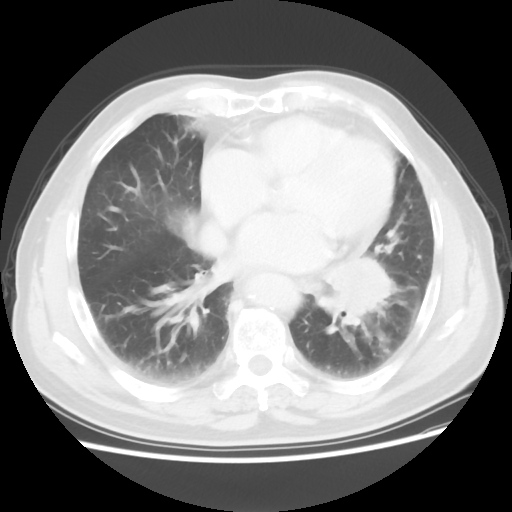
Chest CT, one axial slice; position 25 of 56 along the scan axis; reconstruction kernel STANDARD; lung window (W 1500 / L -600 HU); 5 mm slice thickness; 512 × 512 image matrix, field of view 360 × 360 mm. Male patient, age 75 years. Case-level facts recorded for this patient, not image findings: clinical TNM (as recorded): T3 N0 M0.
Annotated regions visible in this slice (bounding box drawn by a radiologist):
- lung tumour (recorded histology: squamous cell carcinoma): box from (x=313, y=244) to (x=408, y=336) px